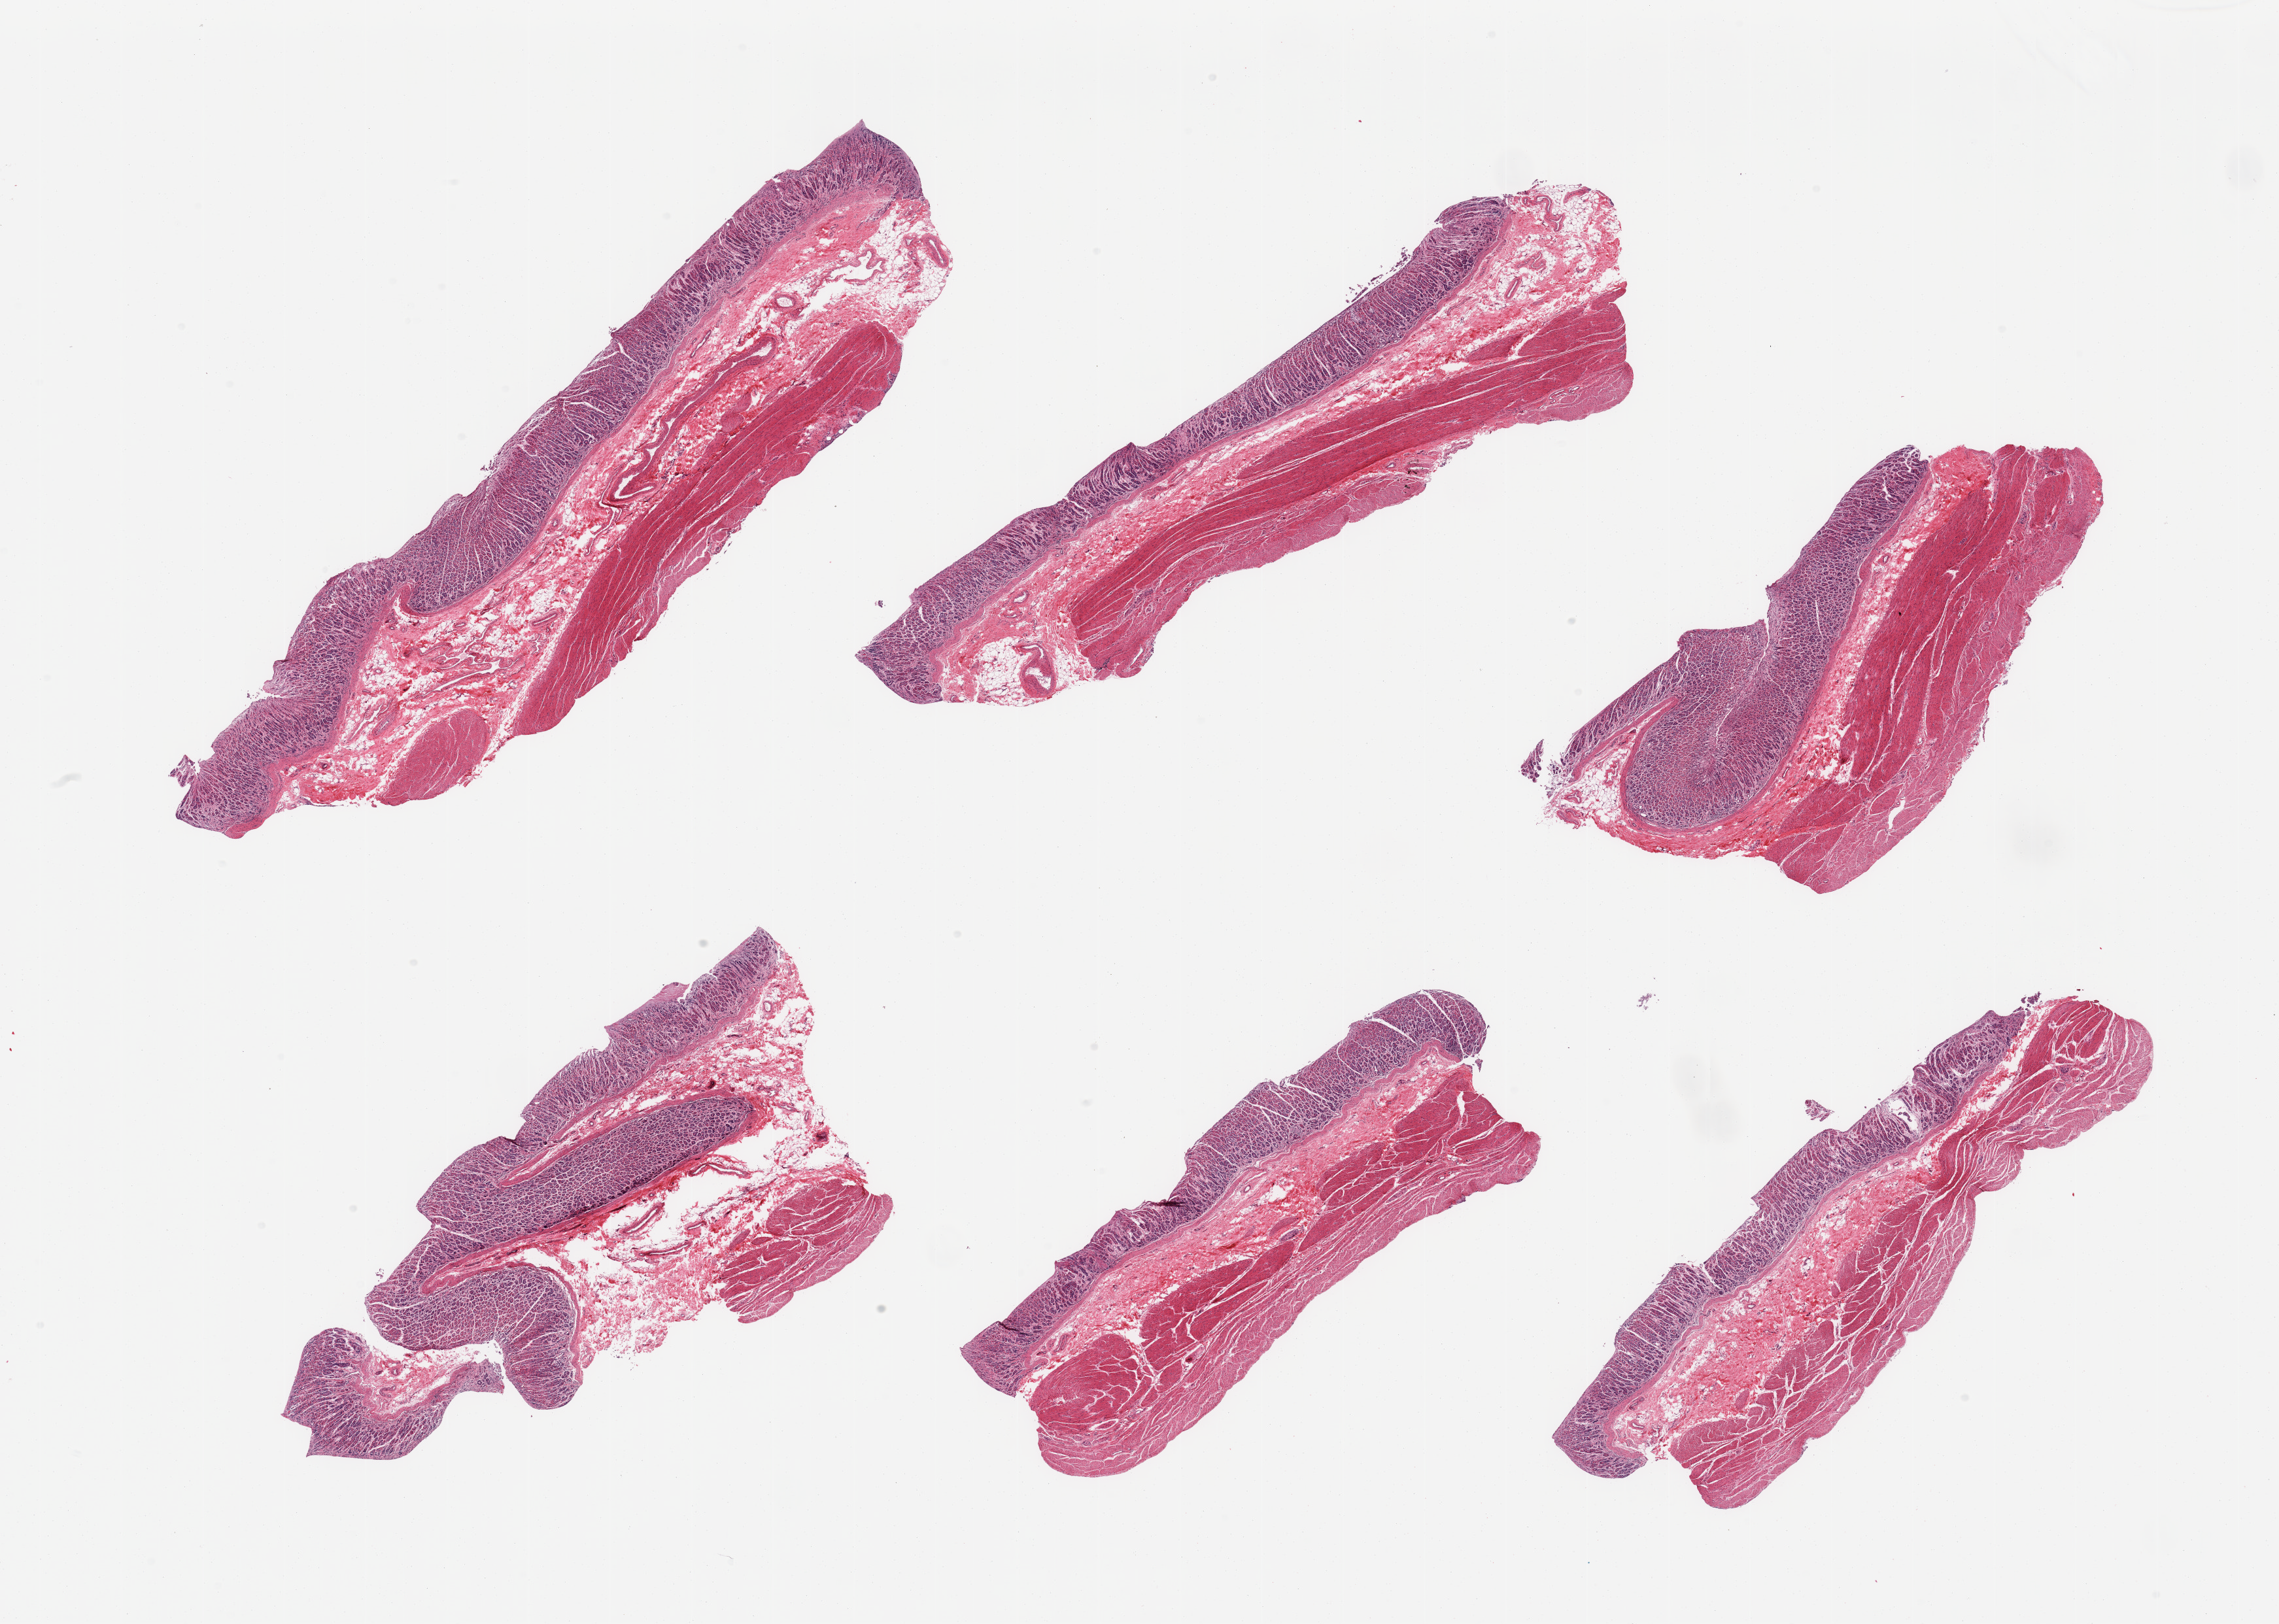
Digitized H&E-stained section, low-resolution overview of the scanned area, about 27.6 x 19.6 mm, PAXgene-fixed paraffin-embedded (PFPE) section, sampled site (target tissue): stomach, tissue donor sample. Male donor.
• reviewer comment on this tissue sample: 6 pieces; full thickness, mild to moderate autolysis of mucosa, muscularis is better preserved